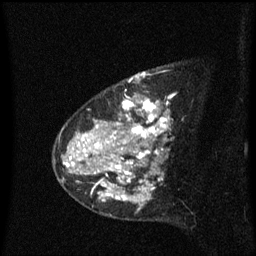
Breast MRI (dynamic contrast-enhanced), one sagittal slice; position 44 of 60 along the scan axis; dynamic contrast-enhanced series, image 2 of 3 at this slice position (ordered by acquisition); 1.5 T; TE 4.2 ms, TR 8.4 ms; 256 × 256 image matrix, field of view 200 × 200 mm. Patient: female, 48 years. Case-level facts recorded for this patient, not image findings: setting: breast cancer imaged before/during neoadjuvant chemotherapy; receptor status: HR-positive, HER2-negative.
Annotated regions visible in this slice (semi-automatically segmented with operator editing):
- analysis volume of interest (the breast-tissue region the enhancement analysis was run in; not a lesion): box from (x=80, y=78) to (x=173, y=221) px
- tumour enhancement mask (voxels above the 70 % enhancement threshold inside the analysis volume of interest): (x=80, y=78)–(x=169, y=207)